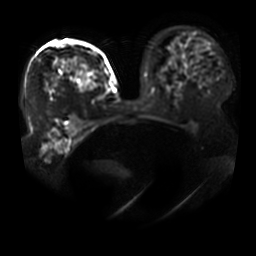
Breast MRI, one axial slice; position 28 of 41 along the scan axis; diffusion-weighted series; image 2 of 4 stored at this slice position (different b-values; order by instance number); 3 T; 256 × 256 image matrix, field of view 400 × 400 mm. Female patient.
Structures marked on this image (expert manual segmentation):
- tumour on diffusion-weighted imaging: box from (x=61, y=57) to (x=95, y=91) px